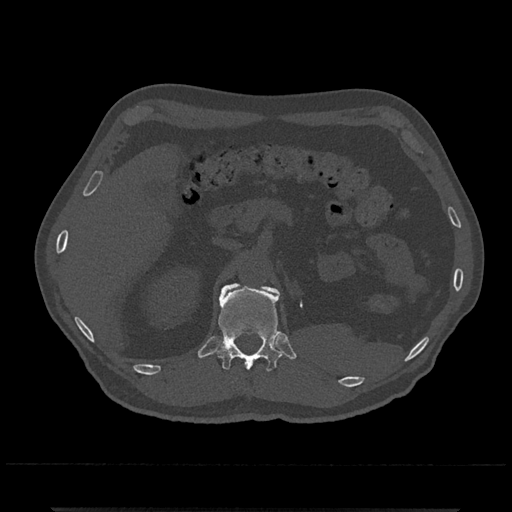
CT including the spine, one axial slice; position 426 of 797 along the scan axis; bone window (W 1800 / L 400 HU); 0.5 mm slice thickness; 512 × 512 image matrix, field of view 393 × 393 mm. Patient: male, 67 years. Case-level facts recorded for this patient, not image findings: primary cancer: prostate.
Outlined on this slice (semi-automatic segmentation, software-assisted and operator-edited):
- L1 vertebra: bounding box [x1, y1, x2, y2] px = [258, 284, 275, 292]
- T12 vertebra: [215, 283, 282, 372]